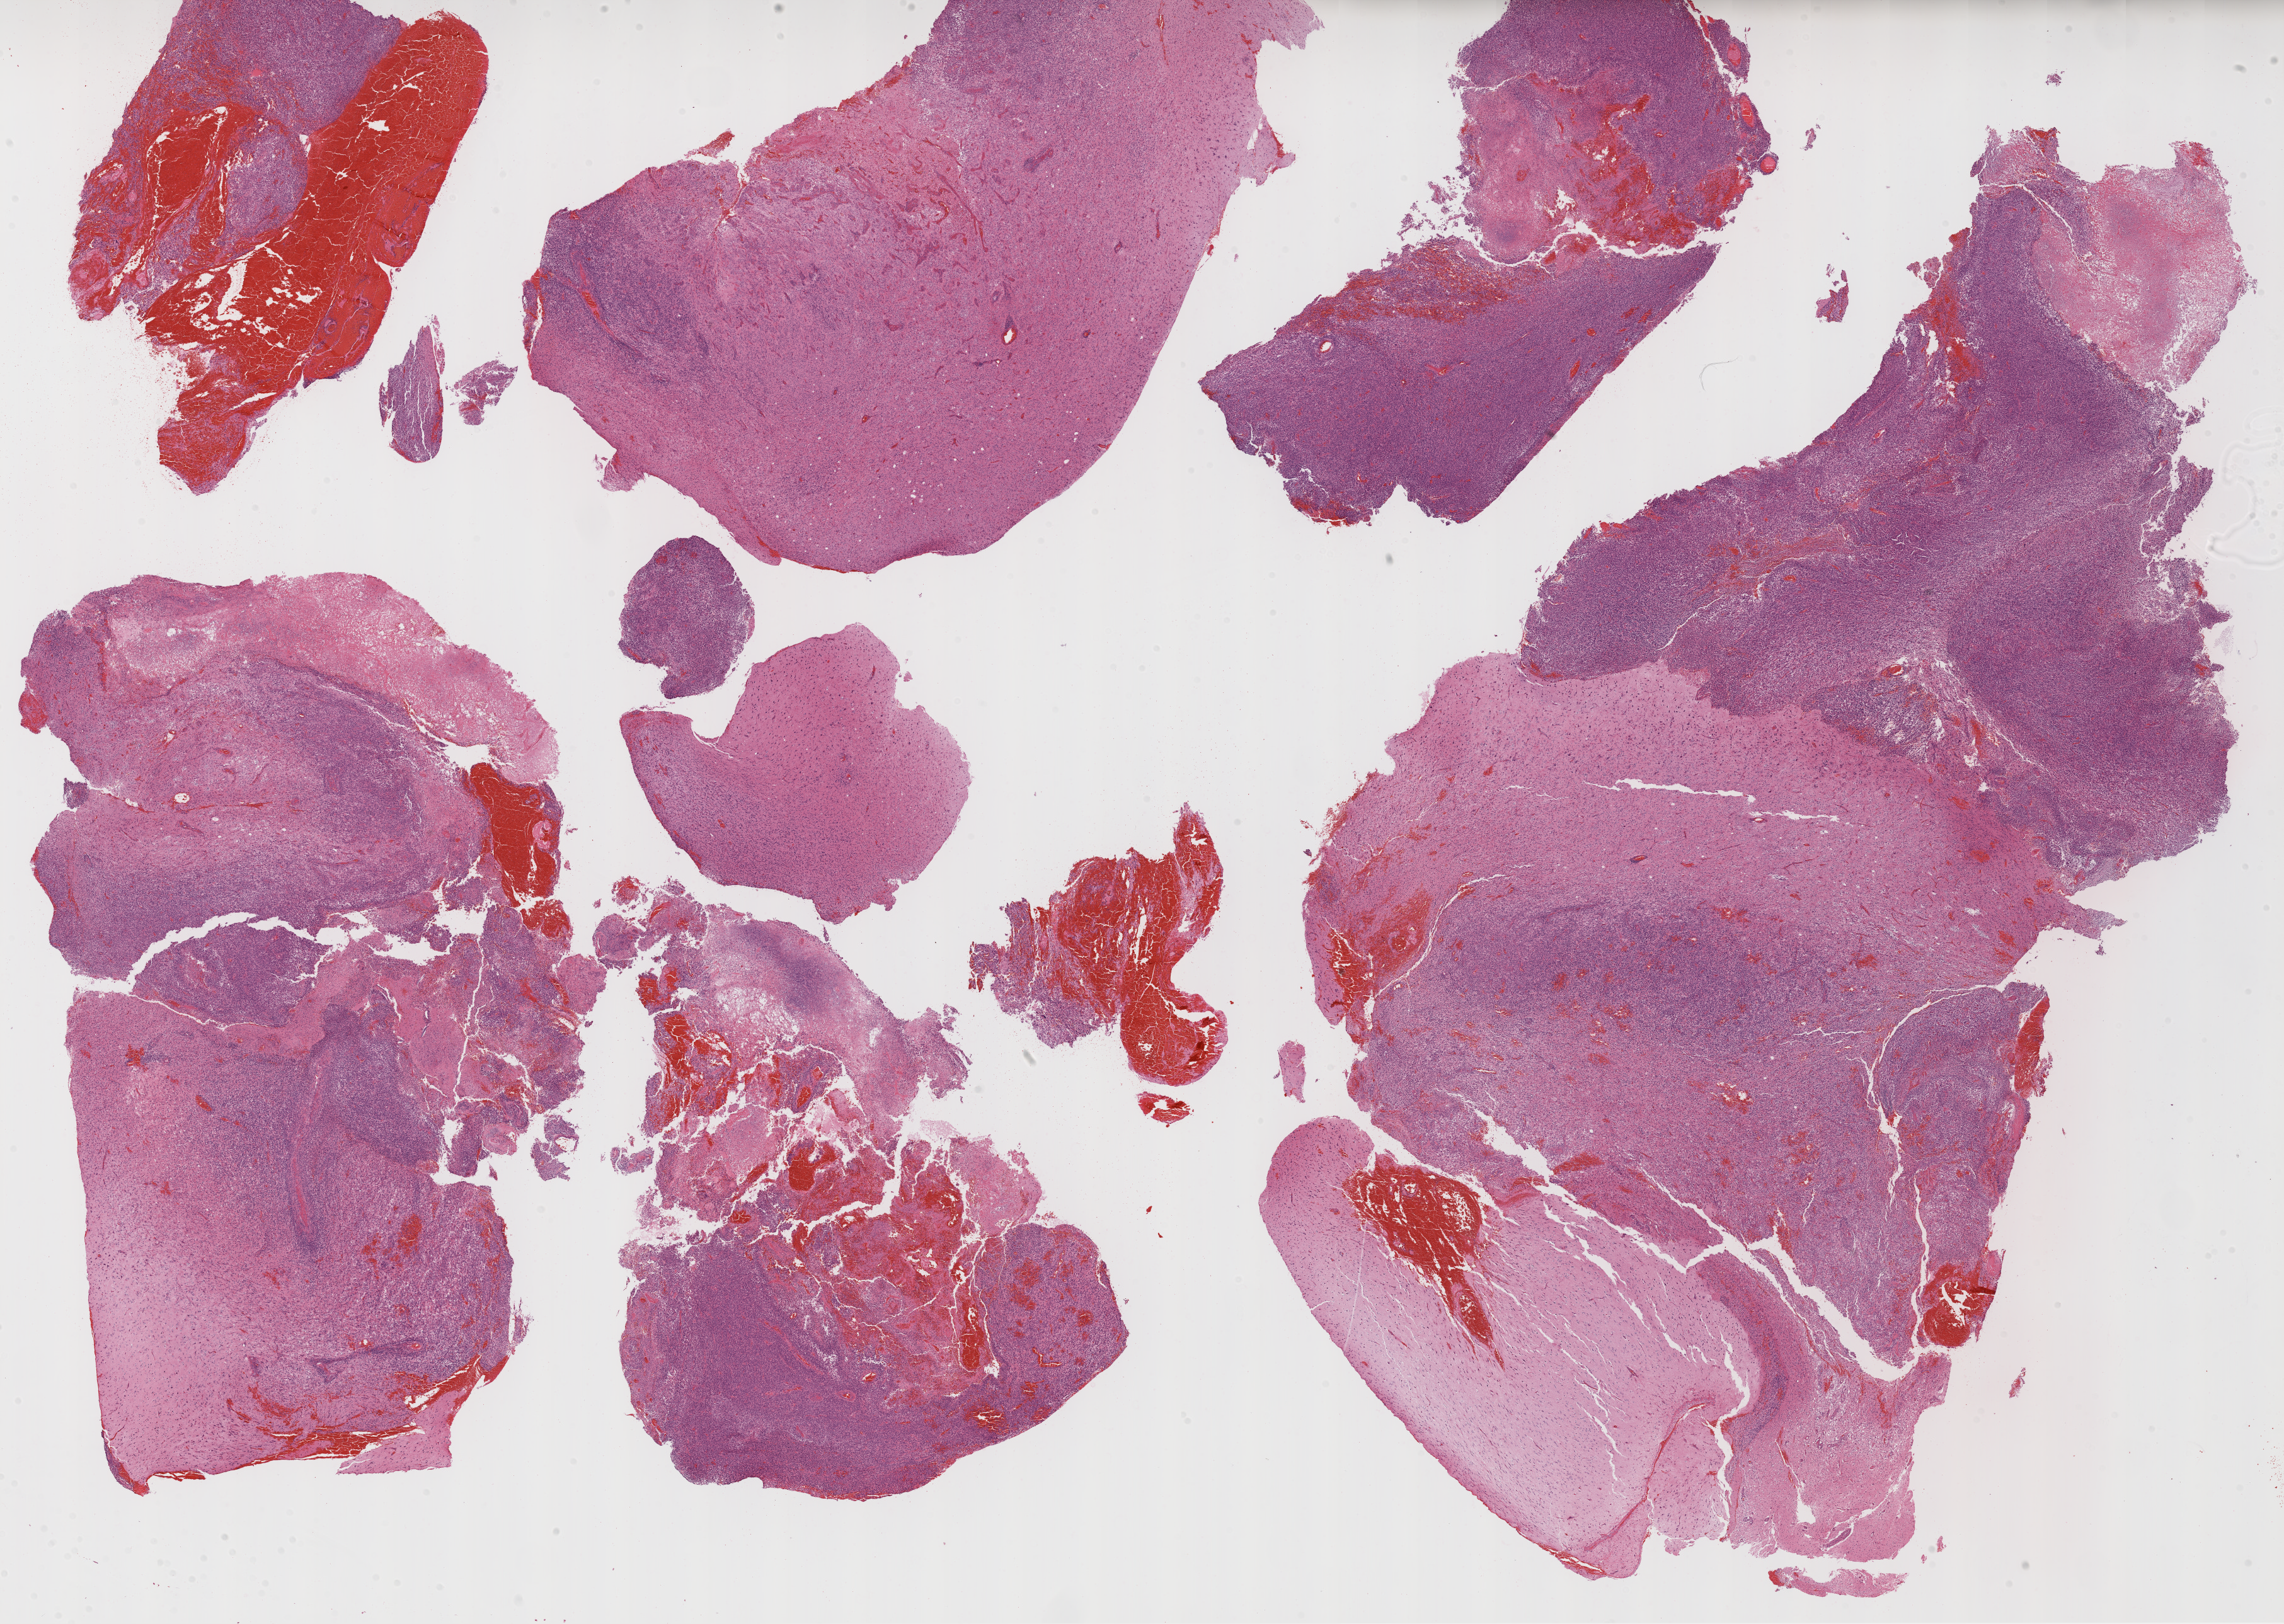
Whole-slide histology image, H&E-stained — shown as a low-resolution overview of the whole scanned area (about 29.1 x 20.7 mm). Formalin-fixed paraffin-embedded (FFPE) diagnostic section. Sample: primary tumour, brain. Patient: female, age at initial diagnosis 59 years.
* diagnosis: Glioblastoma